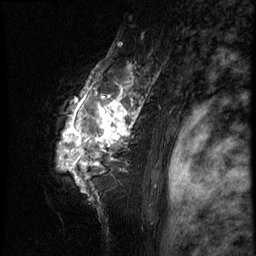
Breast MRI (dynamic contrast-enhanced), one sagittal slice; 3 images stored at this slice position (order not interpretable as contrast timing); 1.5 T; TE 4.2 ms, TR 8.9 ms; 256 × 256 image matrix, field of view 200 × 200 mm. Female patient, age 39 years. Case-level facts recorded for this patient, not image findings: setting: breast cancer imaged before/during neoadjuvant chemotherapy; receptor status: HER2-positive.
Annotated regions visible in this slice (semi-automatic segmentation, software-assisted and operator-edited):
- analysis volume of interest (the breast-tissue region the enhancement analysis was run in; not a lesion): bounding box (x1, y1, x2, y2) in pixels: (45, 44, 166, 196)
- tumour enhancement mask (voxels above the 140 % enhancement threshold inside the analysis volume of interest): (67, 69, 156, 187)